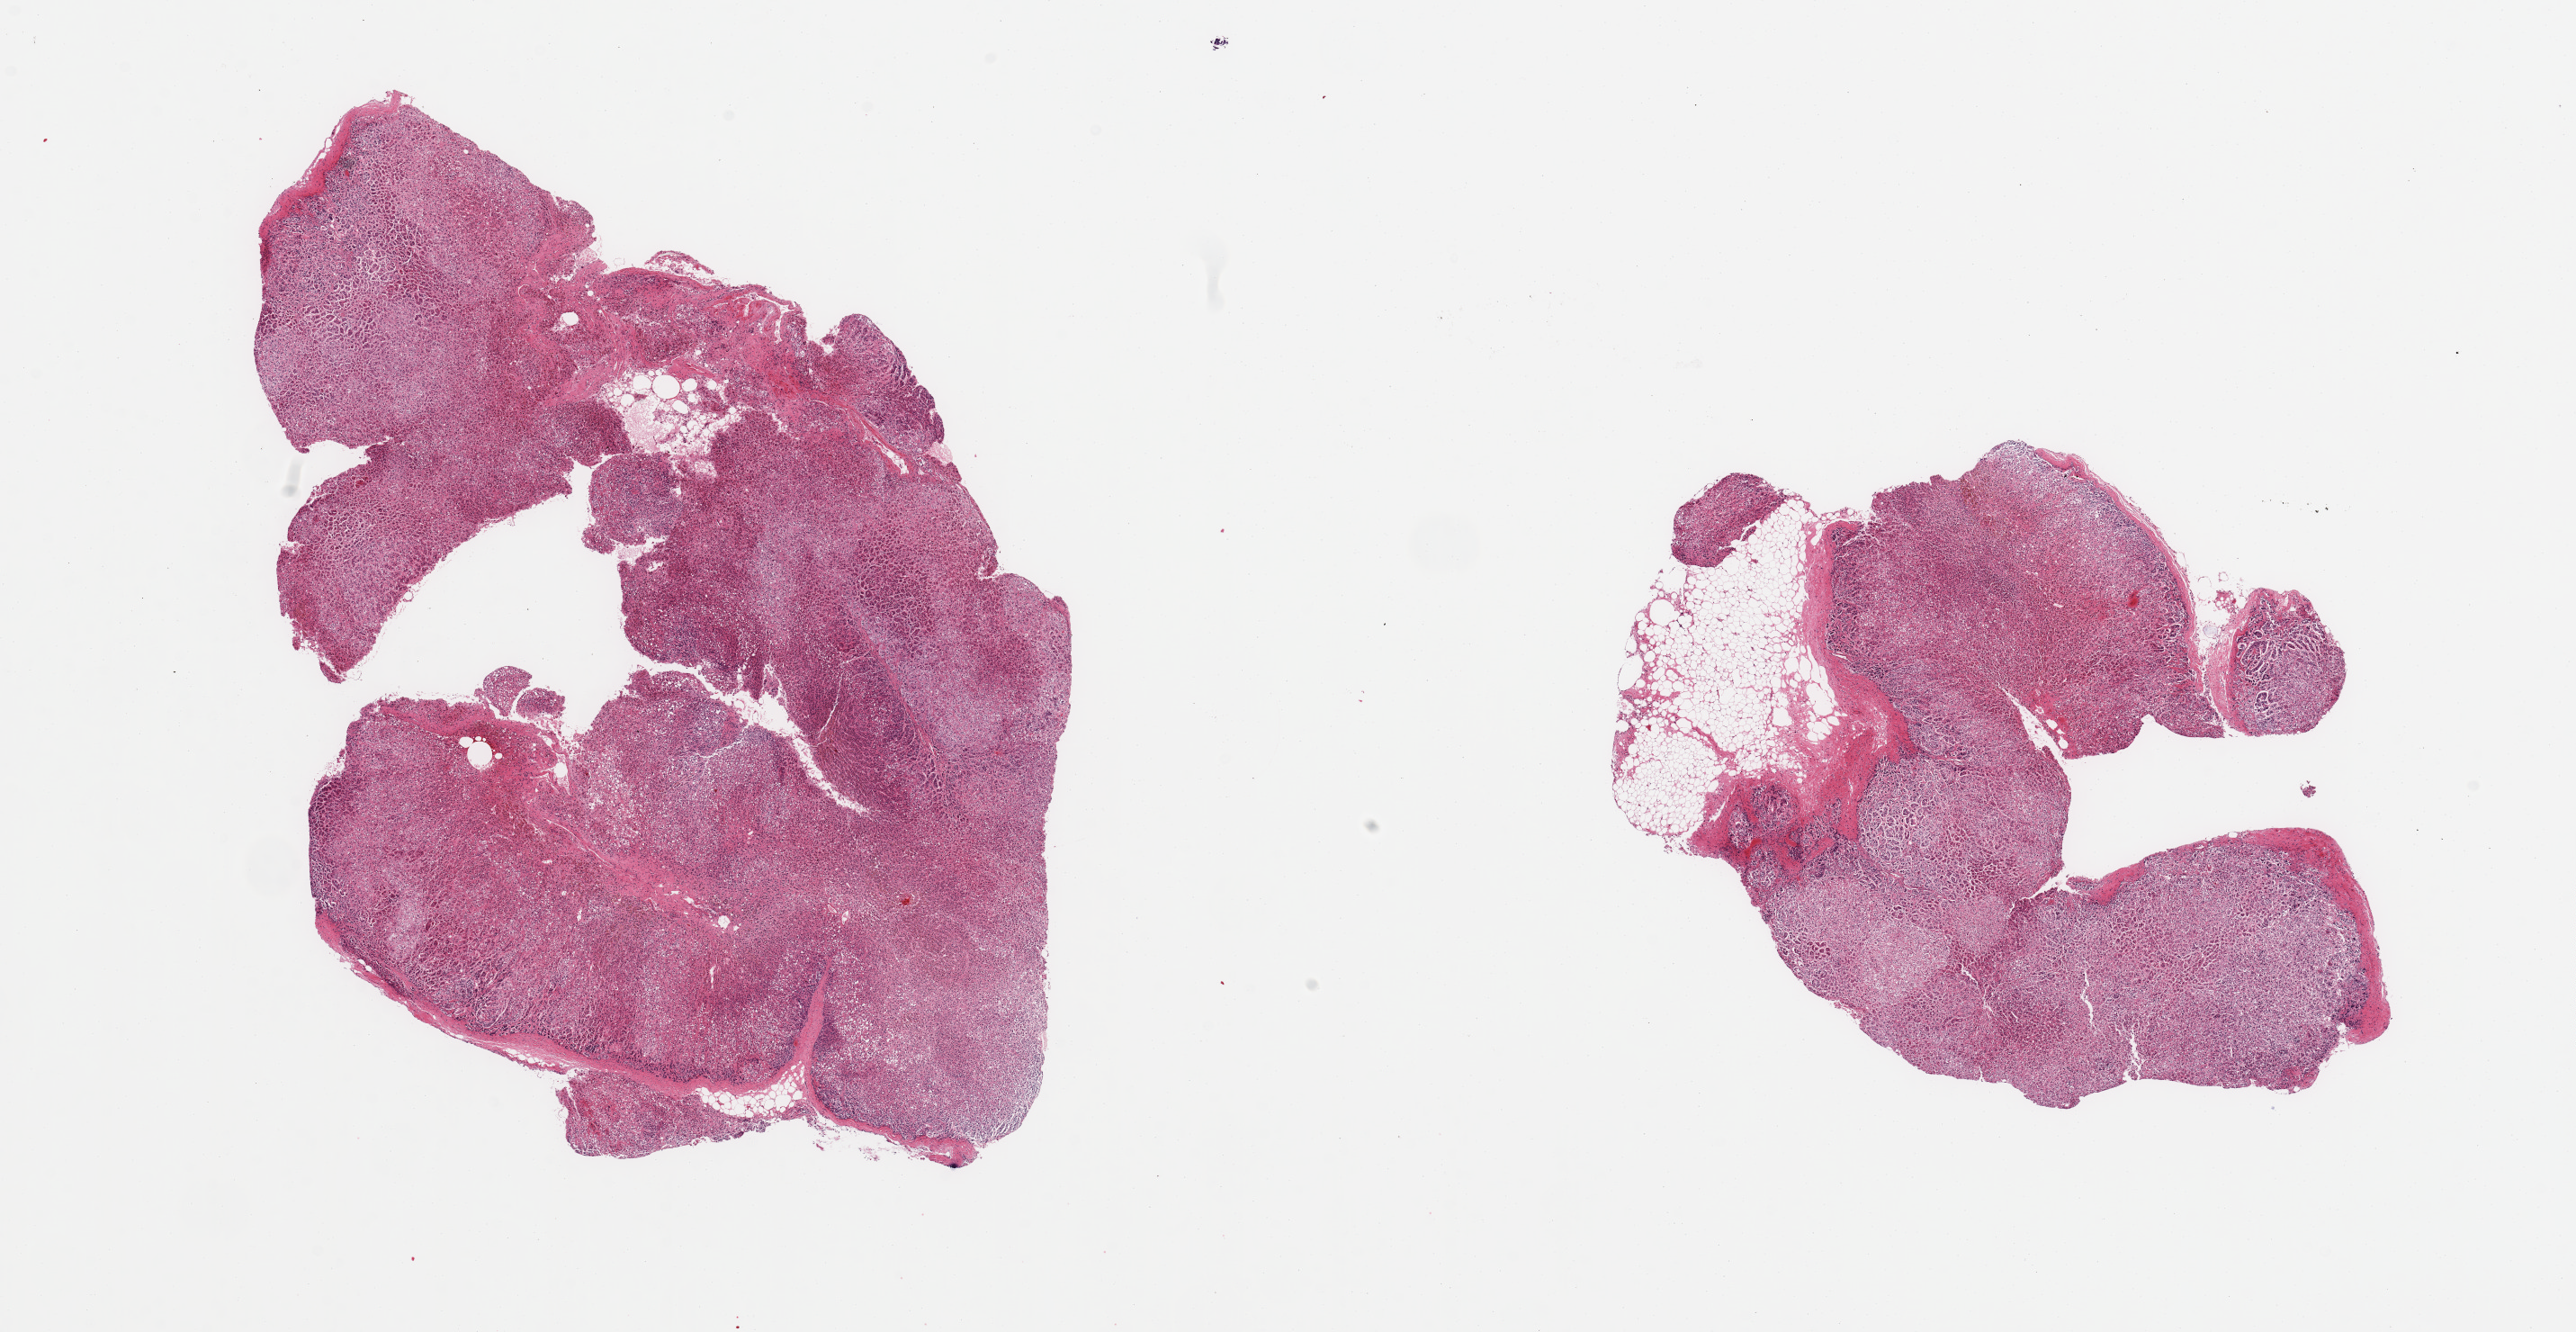
Whole-slide image, haematoxylin and eosin stain, brightfield — whole scanned area (about 22.6 x 11.7 mm, from a 20x scan) shown as a low-resolution overview. PAXgene-fixed, paraffin-embedded tissue. Sampled site (target tissue): adrenal gland. Donor tissue sample. Donor sex: female.
Reviewer comment on this tissue sample: 2 pieces; adrenal cortex, 1 piece includes ~20% attached fat.